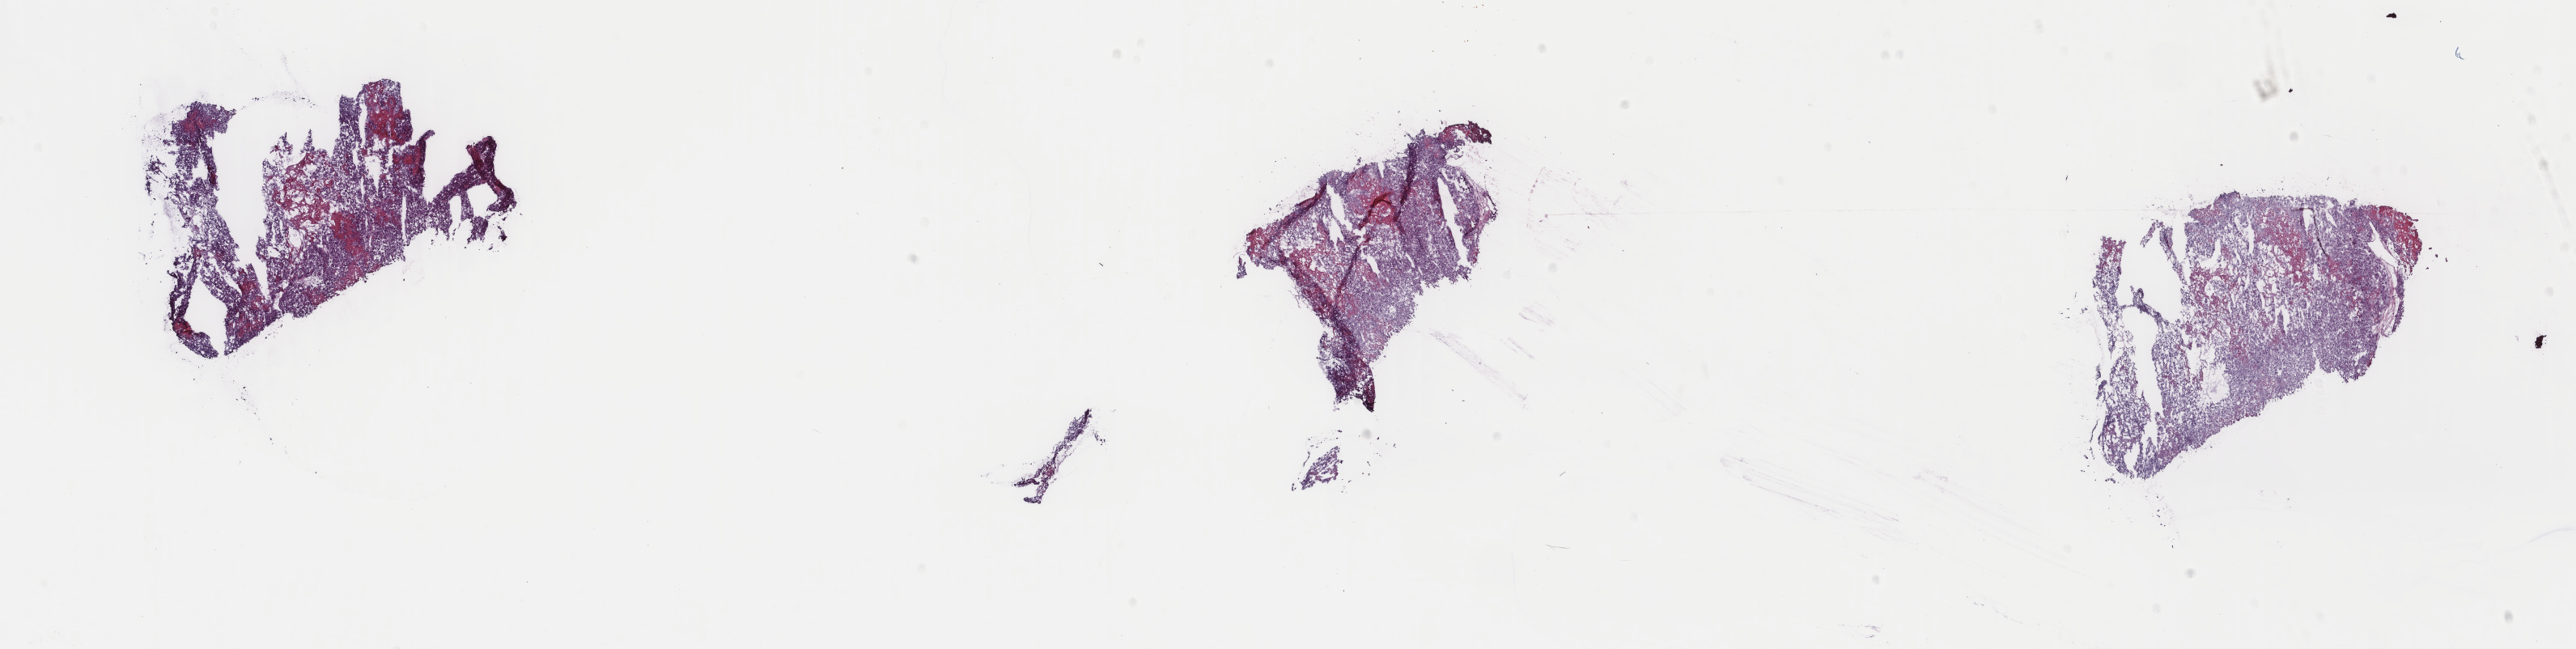
Digitized Hematoxylin and eosin (H&E) stained tissue section (whole slide), low-resolution overview of the scanned area, about 25.3 x 6.4 mm (from a 40x scan), frozen section from the top of the tissue portion, primary tumour sample from the adrenal cortex. Female patient; age at initial diagnosis 29 years. Slide review estimates, as recorded: tumour cells 100%, tumour nuclei 88%, normal cells 0%, stromal cells 0%, necrosis 0%. Infiltration values recorded for this section: lymphocyte infiltration 0%, monocyte infiltration 0%, neutrophil infiltration 0%.
- laterality: right
- pathologic diagnosis: Adrenal cortical carcinoma (cortex of adrenal gland)